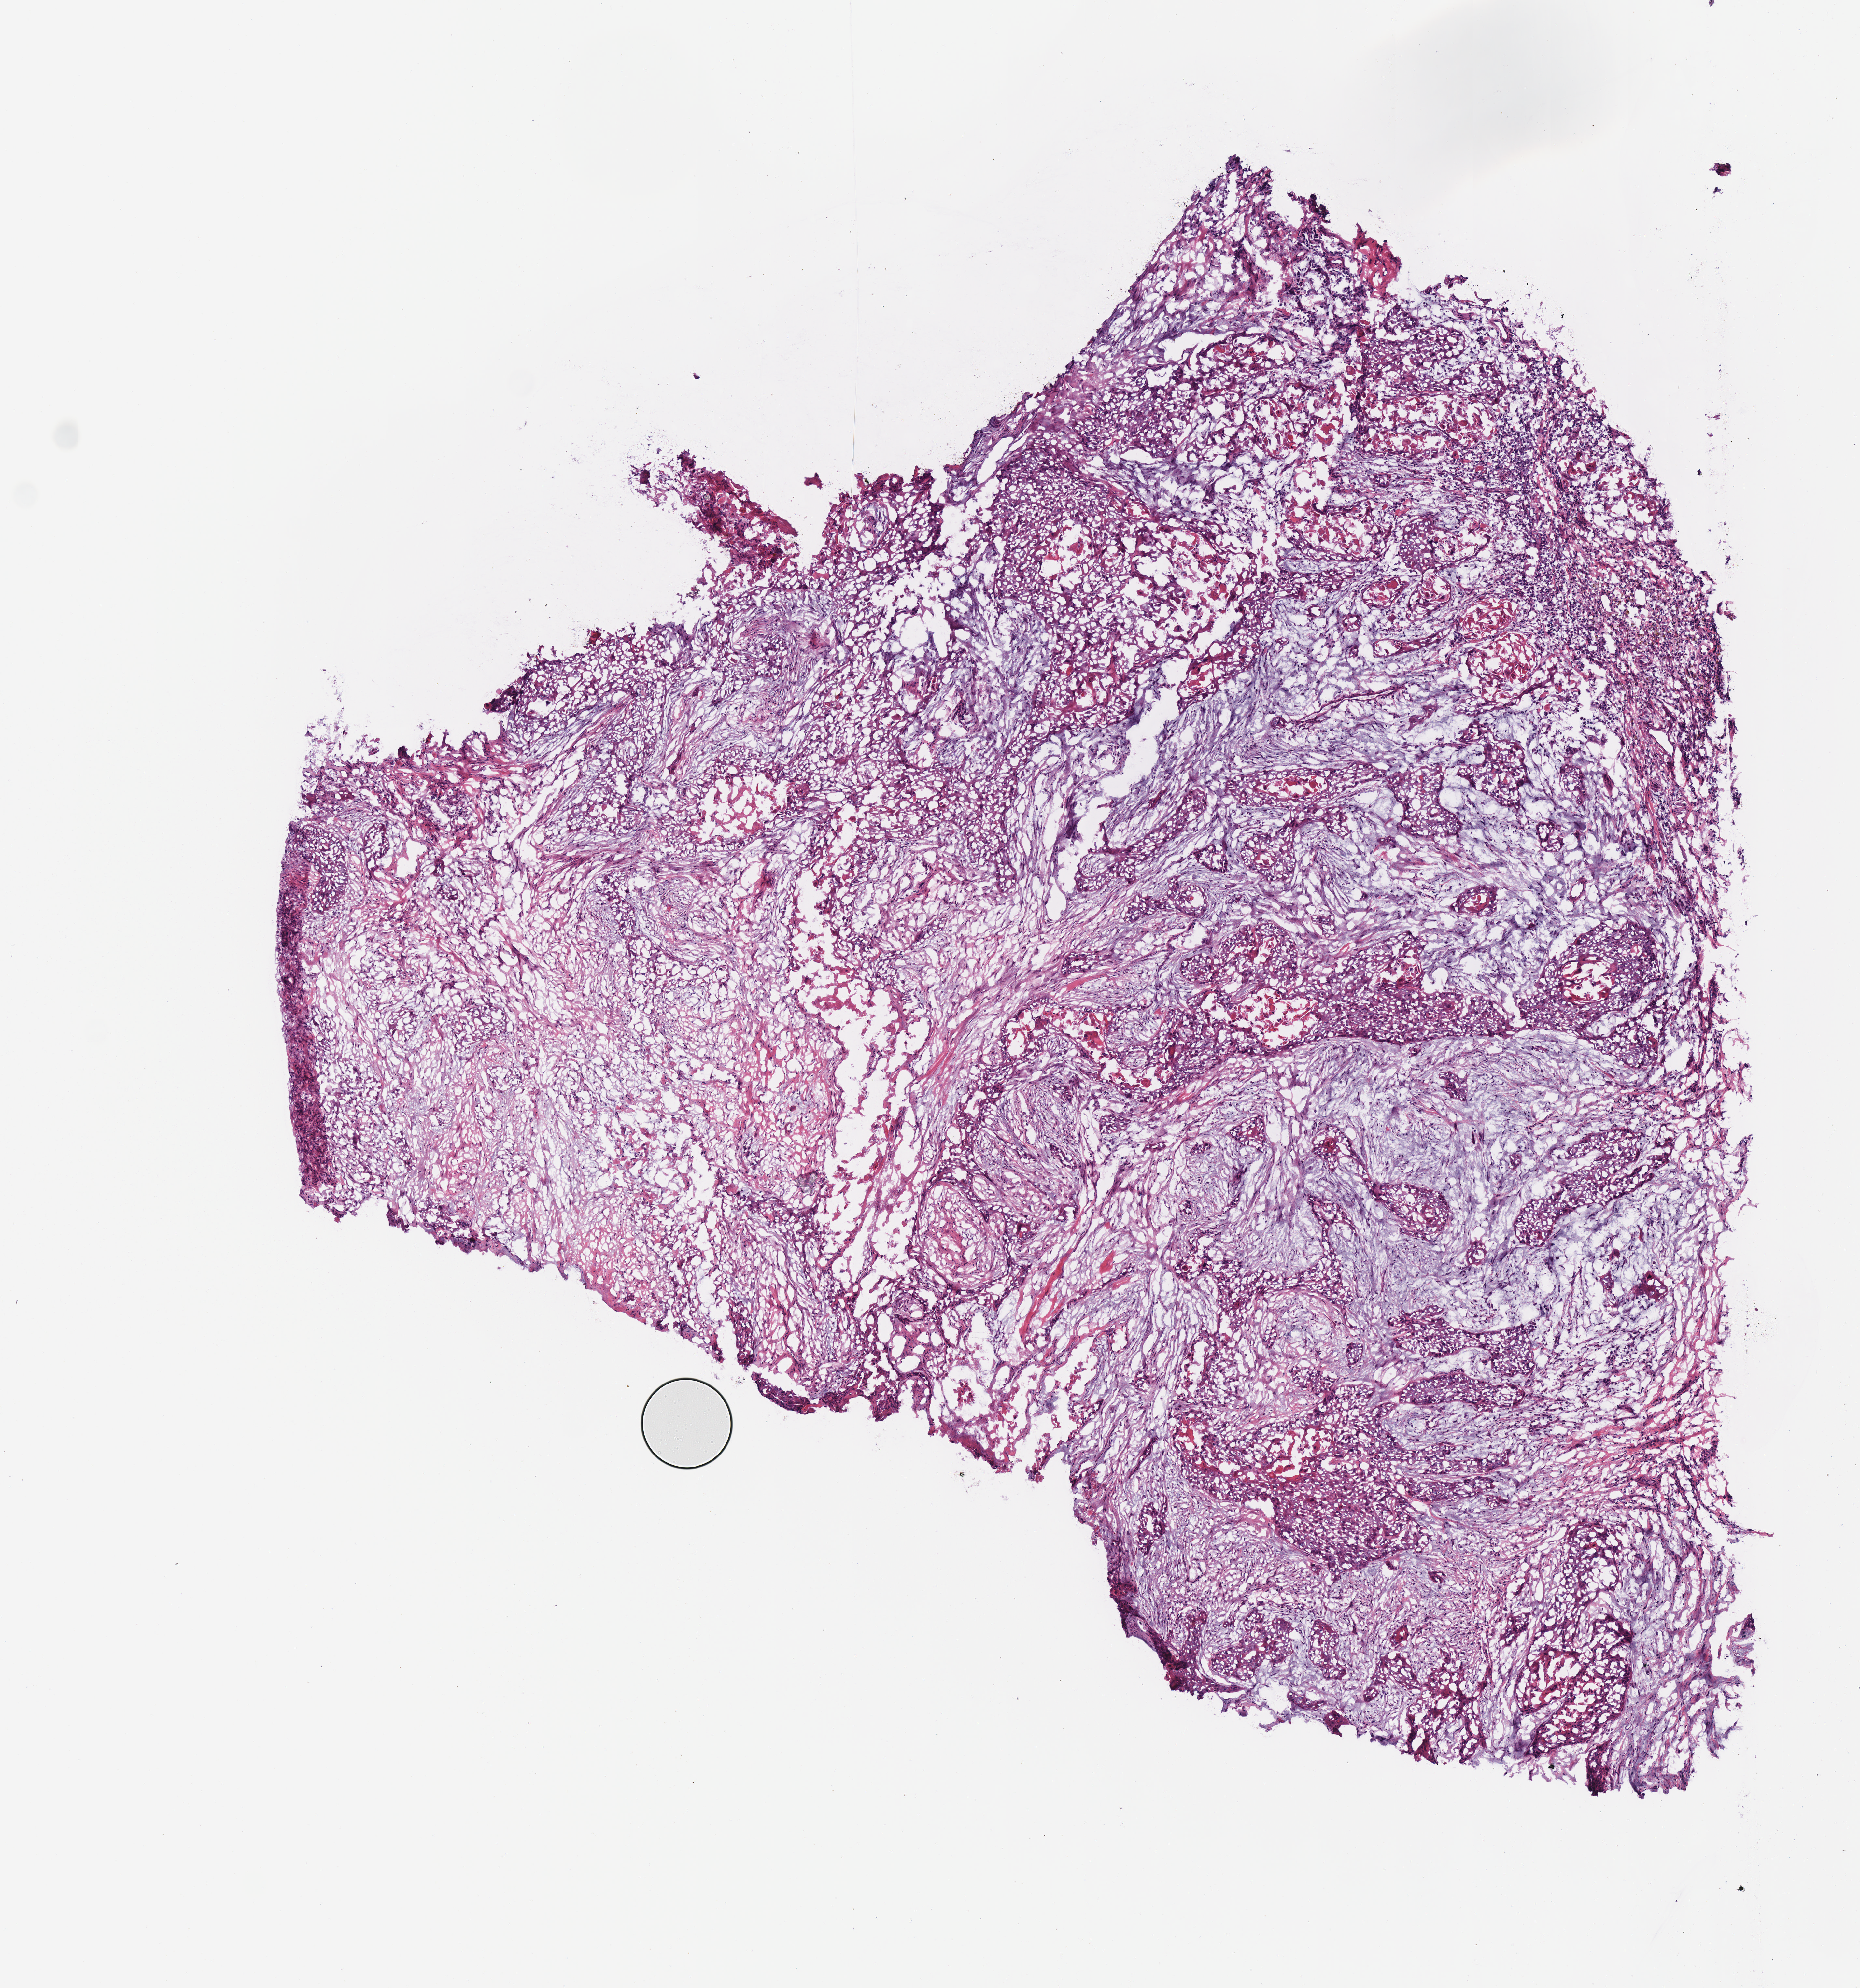
H&E-stained whole-slide image — shown as a low-resolution overview of the whole scanned area (about 5.6 x 6.0 mm, from a 40x scan), frozen section from the top of the tissue portion, primary tumour sample from the head and neck. Patient: male, age at initial diagnosis 76 years. Histologic grade: G2 (moderately differentiated). Composition of this section per pathologist review: tumour cells 100%, tumour nuclei 75%, normal cells 0%, stromal cells 0%, necrosis 0%. Infiltration values recorded for this section: lymphocyte infiltration 2%, monocyte infiltration 0%, neutrophil infiltration 0%.
Pathologic diagnosis: Squamous cell carcinoma, NOS (larynx, NOS). AJCC pathologic stage: IVA (7th edition). Laterality: midline. TNM: T4a N0.